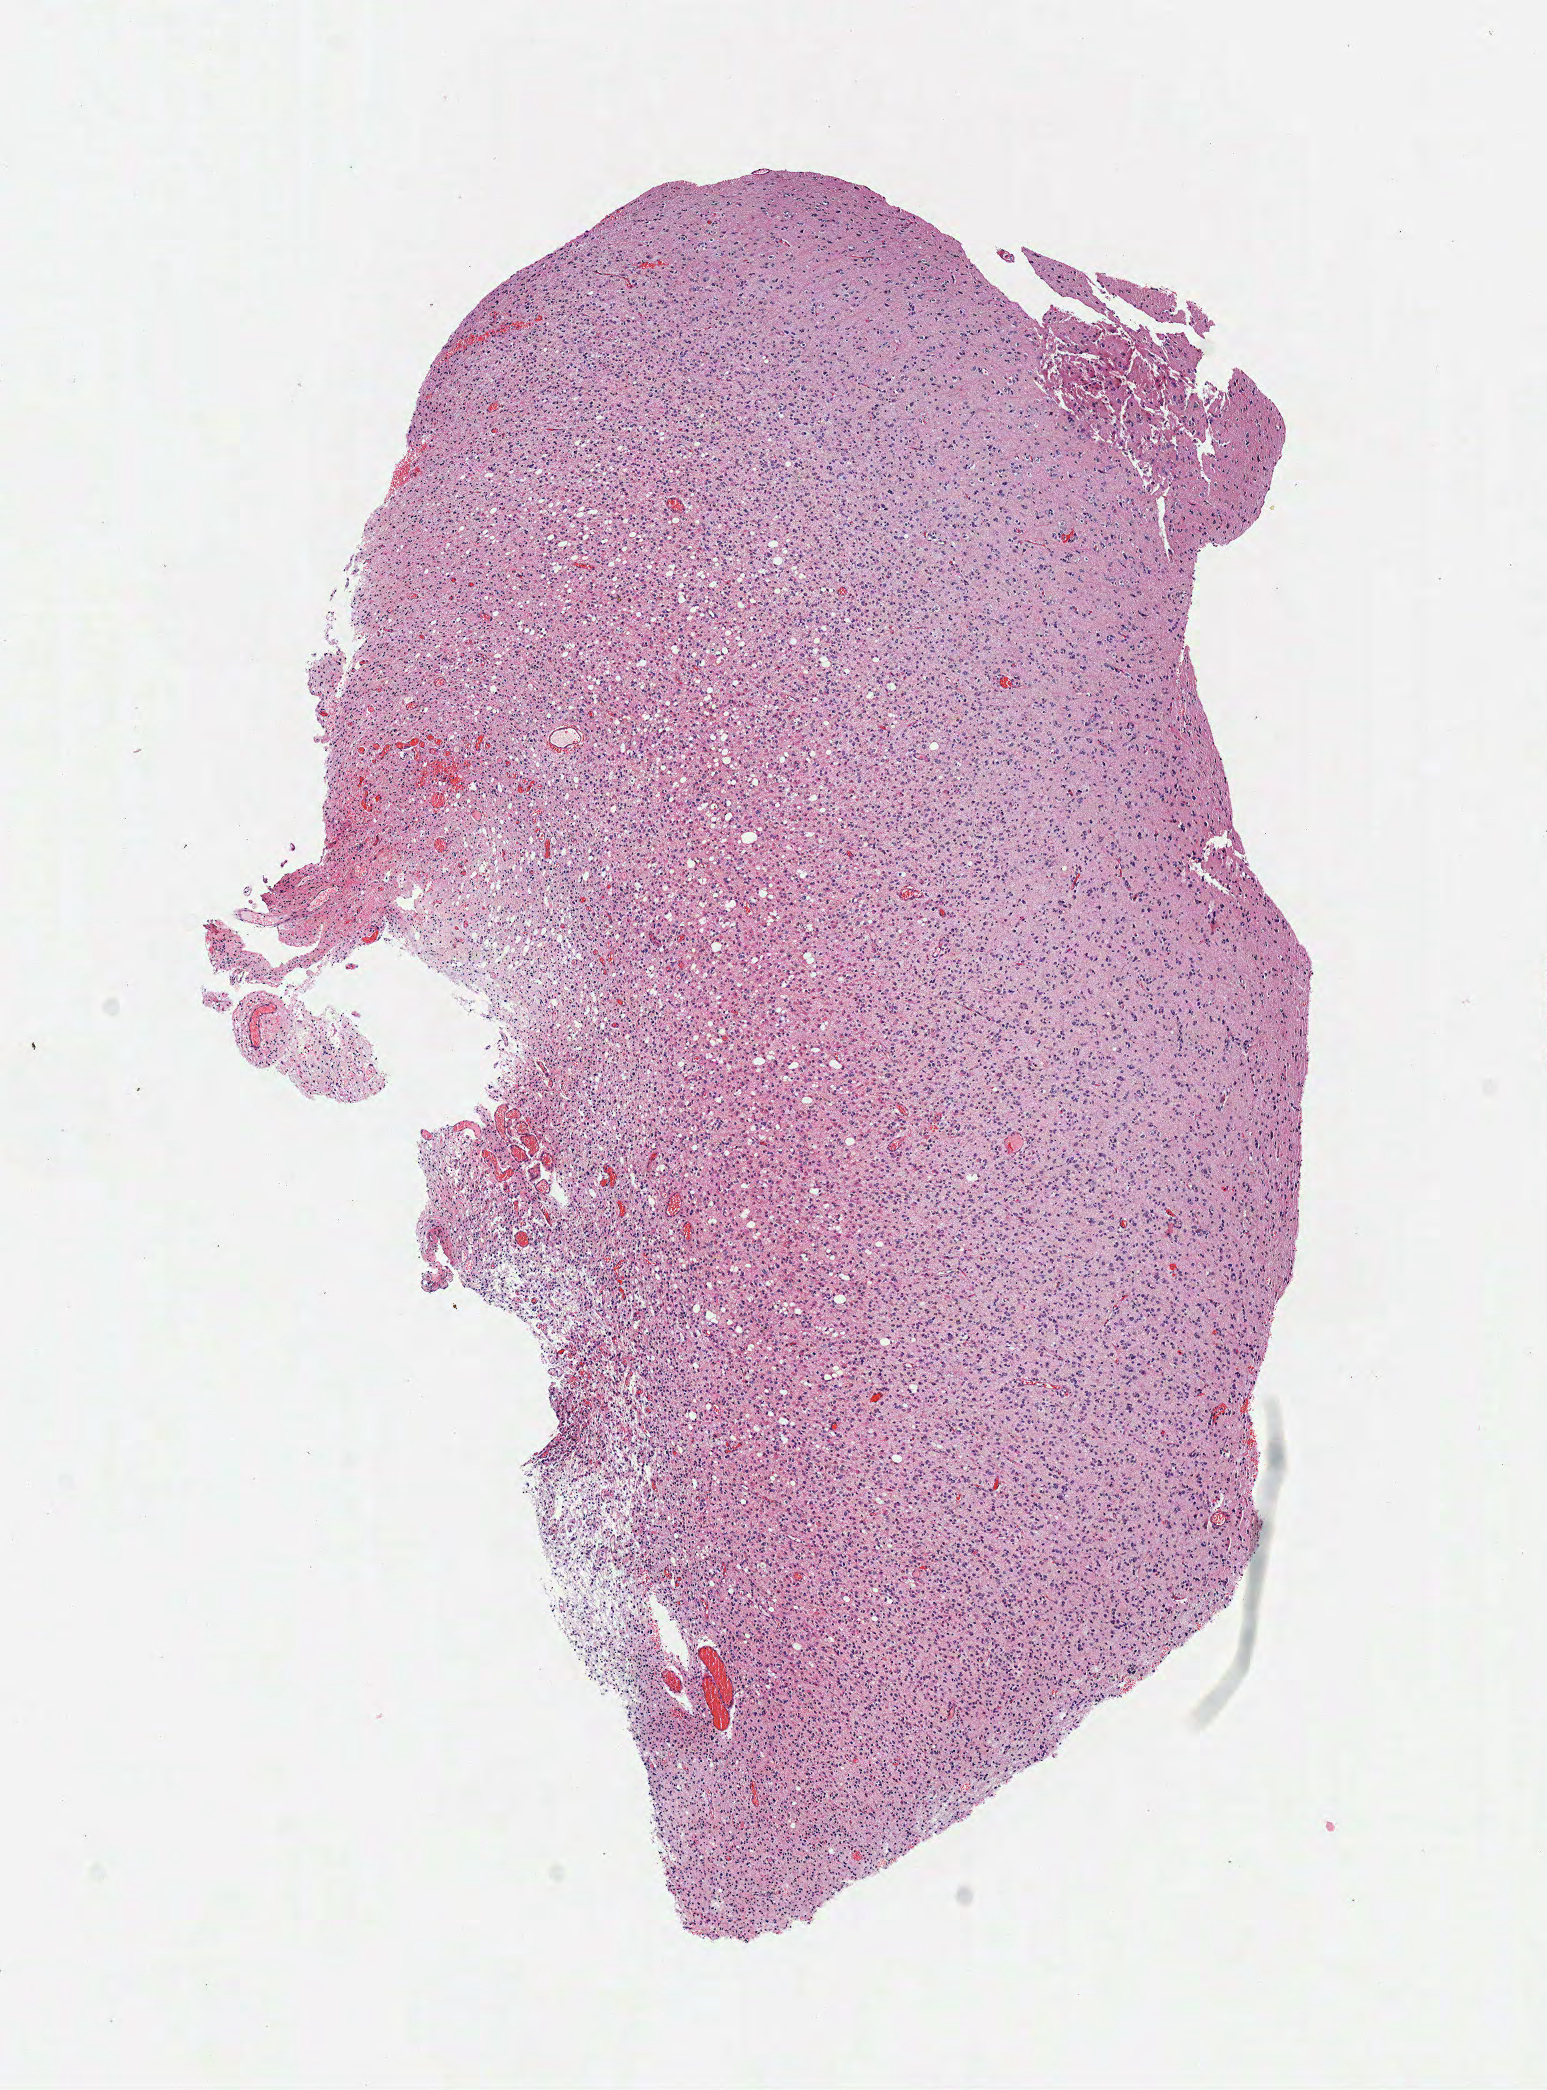
Digitized H&E tissue section (whole slide), shown as a low-resolution overview of the whole scanned area (about 6.1 x 8.2 mm, from a 40x scan), frozen section from the top of the tissue portion, sample: primary tumour, brain. Patient: female, age at initial diagnosis 43 years. Histologic grade: G2 (moderately differentiated). Slide review estimates, as recorded: tumour cells 100%, tumour nuclei 75%, normal cells 0%, stromal cells 0%, necrosis 0%.
Pathologic diagnosis: Mixed glioma.